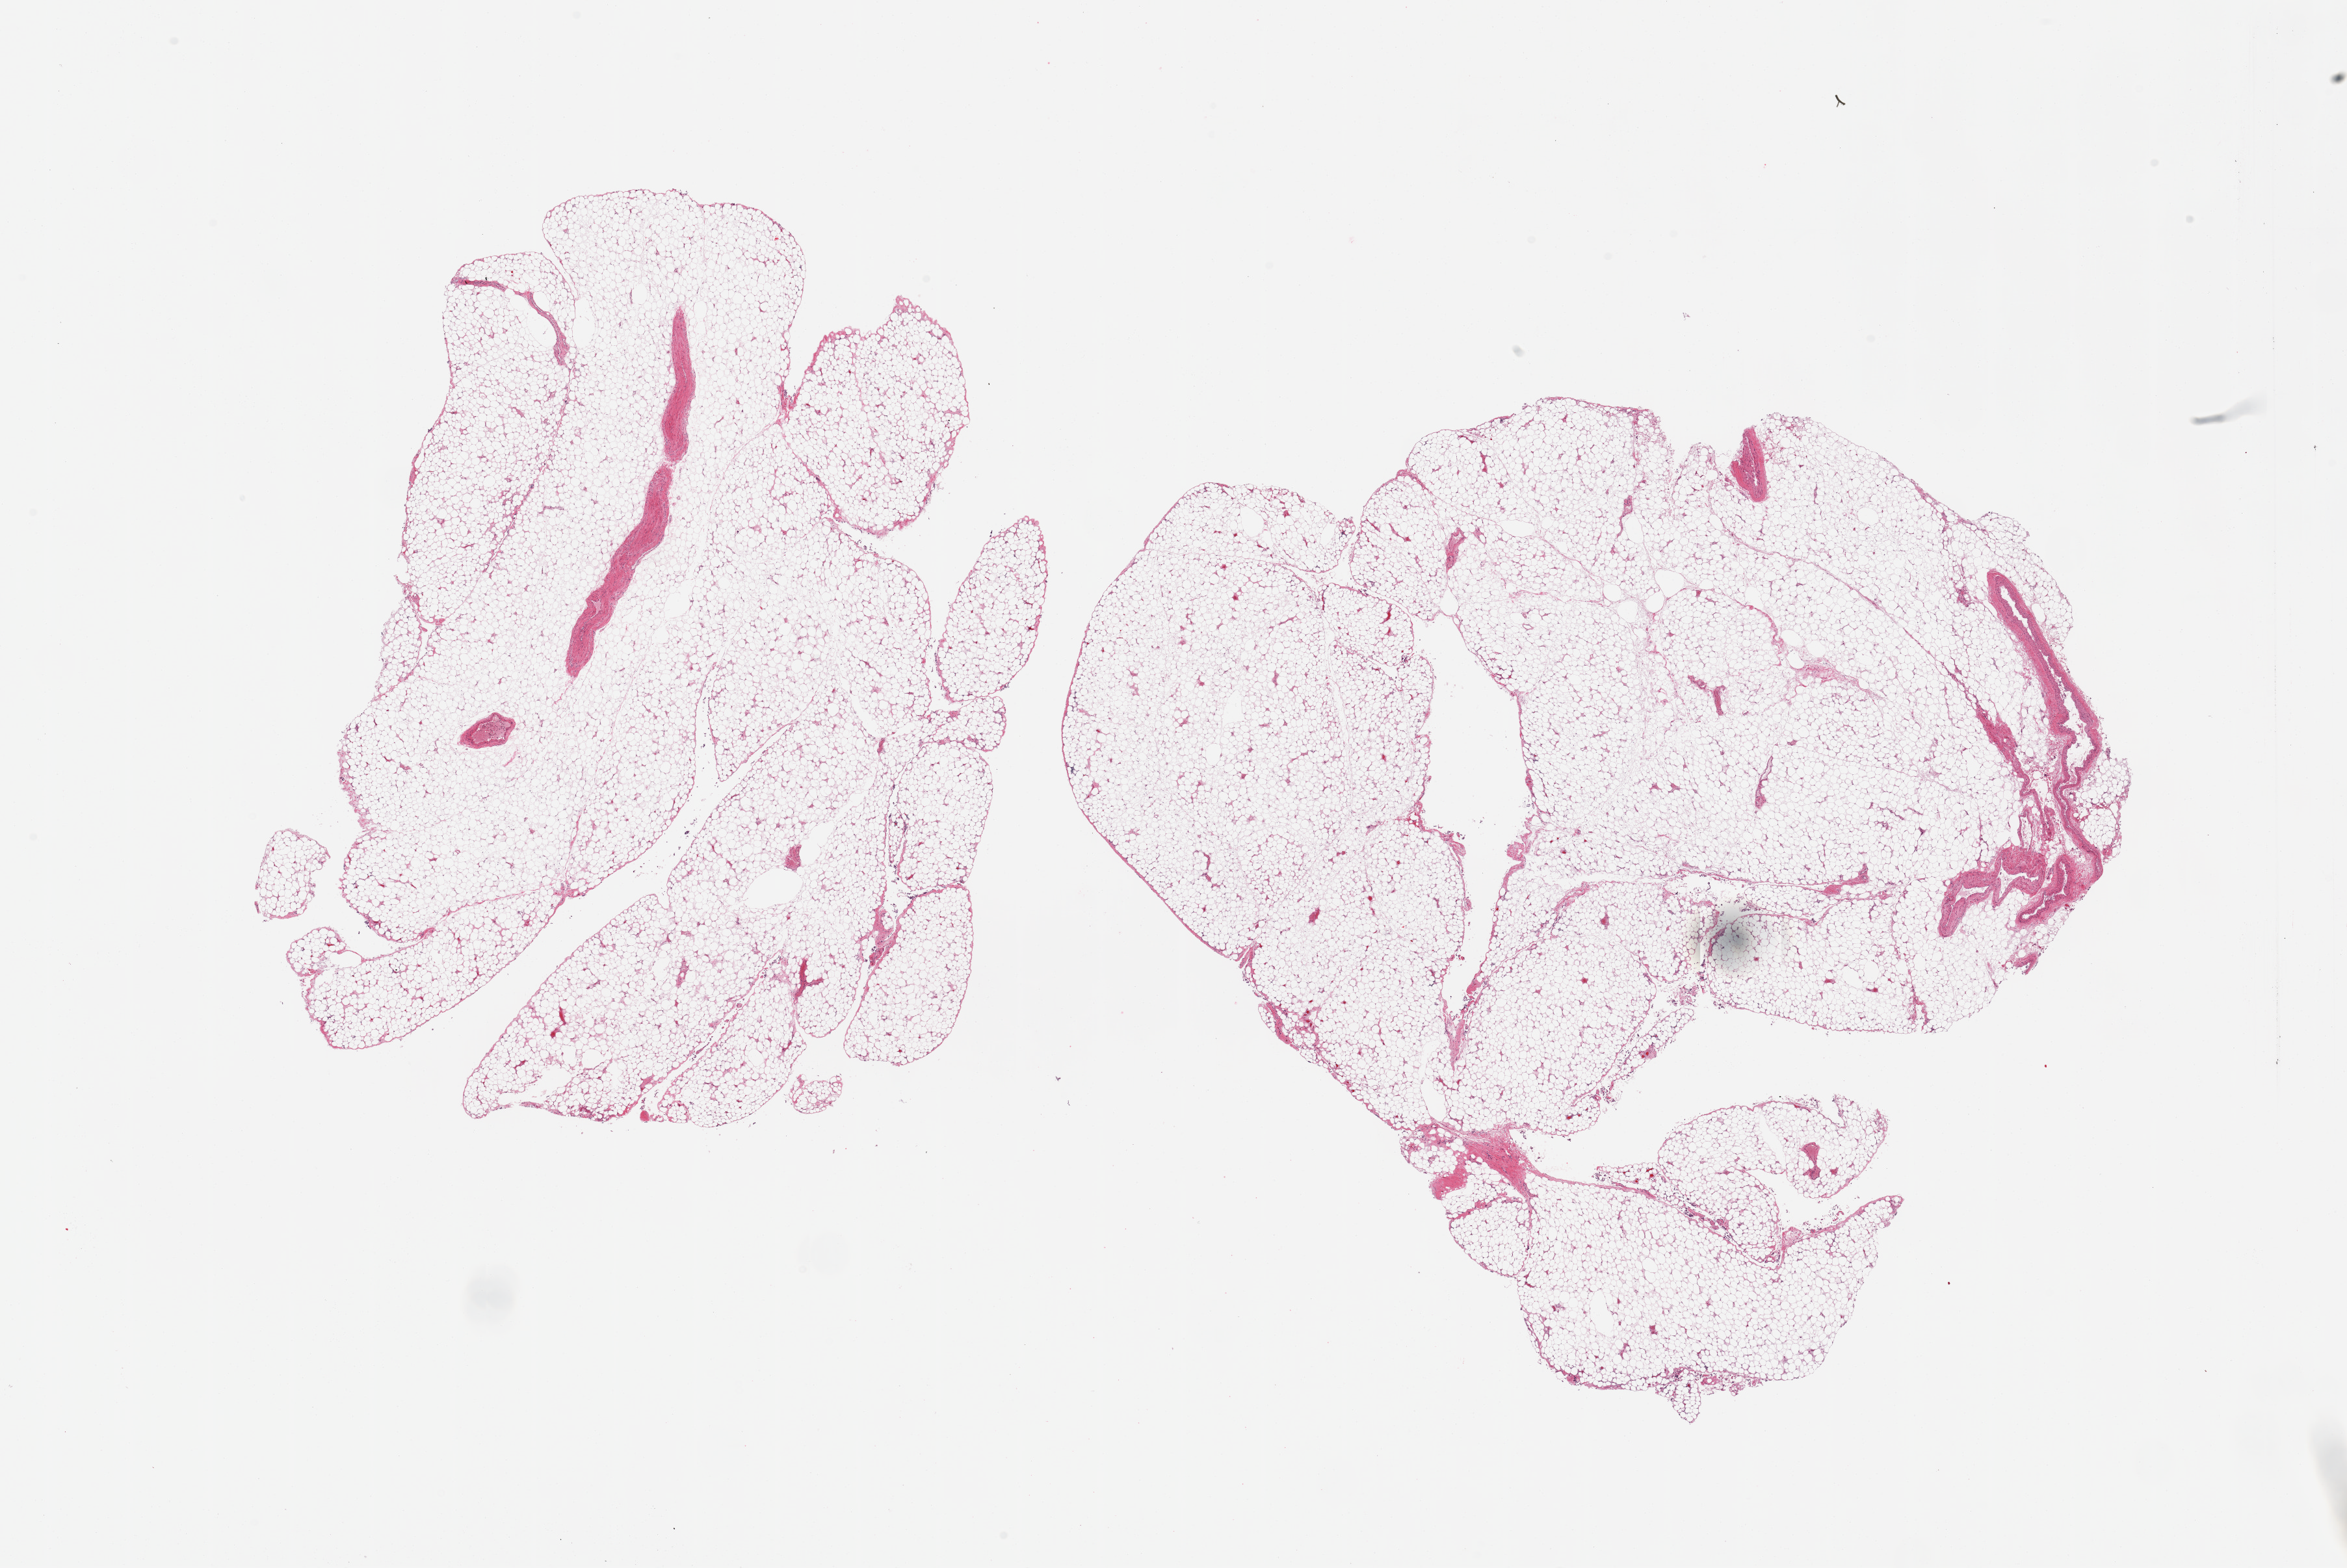
Digitized haematoxylin and eosin-stained section — shown as a low-resolution overview of the whole scanned area (about 28.5 x 19.1 mm, acquisition: 20x scan). PAXgene-fixed, paraffin-embedded tissue. Section of omentum (target tissue). Tissue donor sample. Donor: male.
Review note (as recorded): 2 pieces, peripheral nerve and vascular elements, ~5% of tissue.